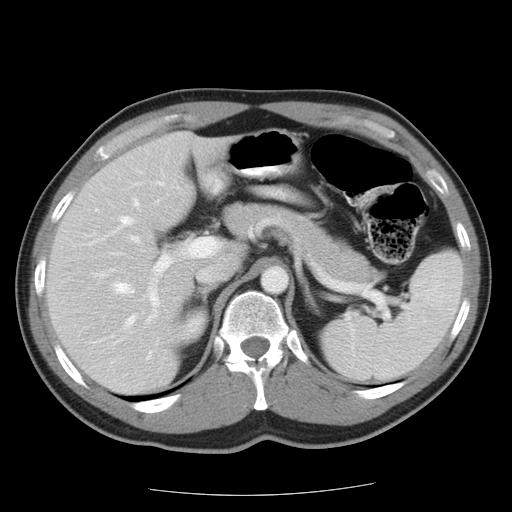
Contrast-enhanced abdominal CT, one axial slice; position 12 of 22 along the scan axis; reconstruction kernel STANDARD; 120 kVp; intravenous contrast given; soft-tissue window (W 400 / L 40 HU); 7.5 mm slice thickness; 512 × 512 image matrix, field of view 359 × 359 mm. Male patient, age 41 years. Case-level facts recorded for this patient, not image findings: diagnosis: colorectal cancer liver metastases, imaged before liver resection; multiple liver metastases: no; largest metastasis: 2.7 cm; disease in both lobes: no.
Annotated regions visible in this slice (expert manual segmentation):
- hepatic veins: bounding box [x1, y1, x2, y2] px = [115, 200, 139, 327]
- liver: [48, 135, 218, 390]
- planned liver remnant (the part of the liver to remain after resection): [48, 136, 217, 351]
- portal vein (with intrahepatic branches): [131, 183, 223, 321]